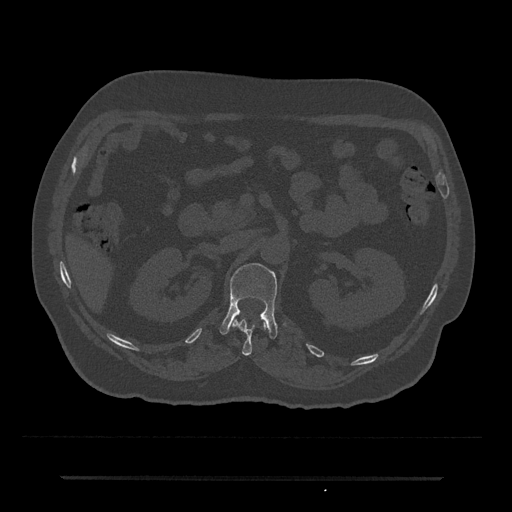
CT including the spine, one axial slice; 120 kVp; bone window (W 1800 / L 400 HU); 512 × 512 image matrix, field of view 437 × 437 mm. Male patient, age 69 years. Case-level facts recorded for this patient, not image findings: primary cancer: prostate.
Outlined on this slice (semi-automatically segmented with operator editing):
- L1 vertebra: bounding box <219,263,277,339> (left, top, right, bottom; pixels)
- T12 vertebra: <231,315,267,356>